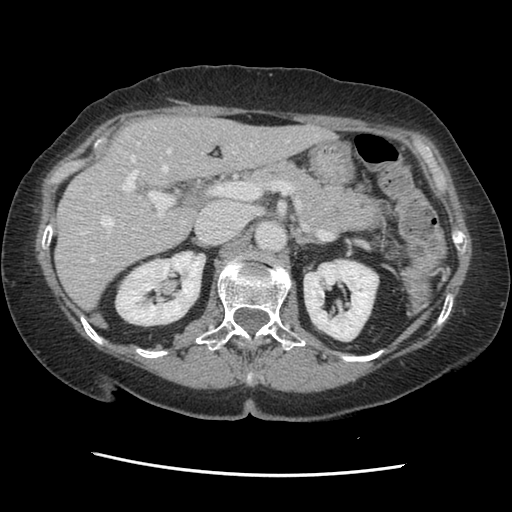
Contrast-enhanced abdominal CT, one axial slice; slice 82 of 141 in the series (ordered by position); 120 kVp; soft-tissue window (W 400 / L 40 HU); 2.5 mm slice thickness; 512 × 512 image matrix, field of view 330 × 330 mm. Female patient, age 61 years. From the clinical record (not read from this slice): diagnosis: colorectal cancer liver metastases, imaged before liver resection; multiple liver metastases: no; largest metastasis: 2.4 cm; disease in both lobes: no.
Outlined on this slice (manually delineated by an expert):
- hepatic veins: bounding box (x1, y1, x2, y2) in pixels: (90, 140, 289, 262)
- liver: (57, 117, 326, 308)
- planned liver remnant (the part of the liver to remain after resection): (57, 117, 326, 308)
- portal vein (with intrahepatic branches): (93, 155, 260, 217)